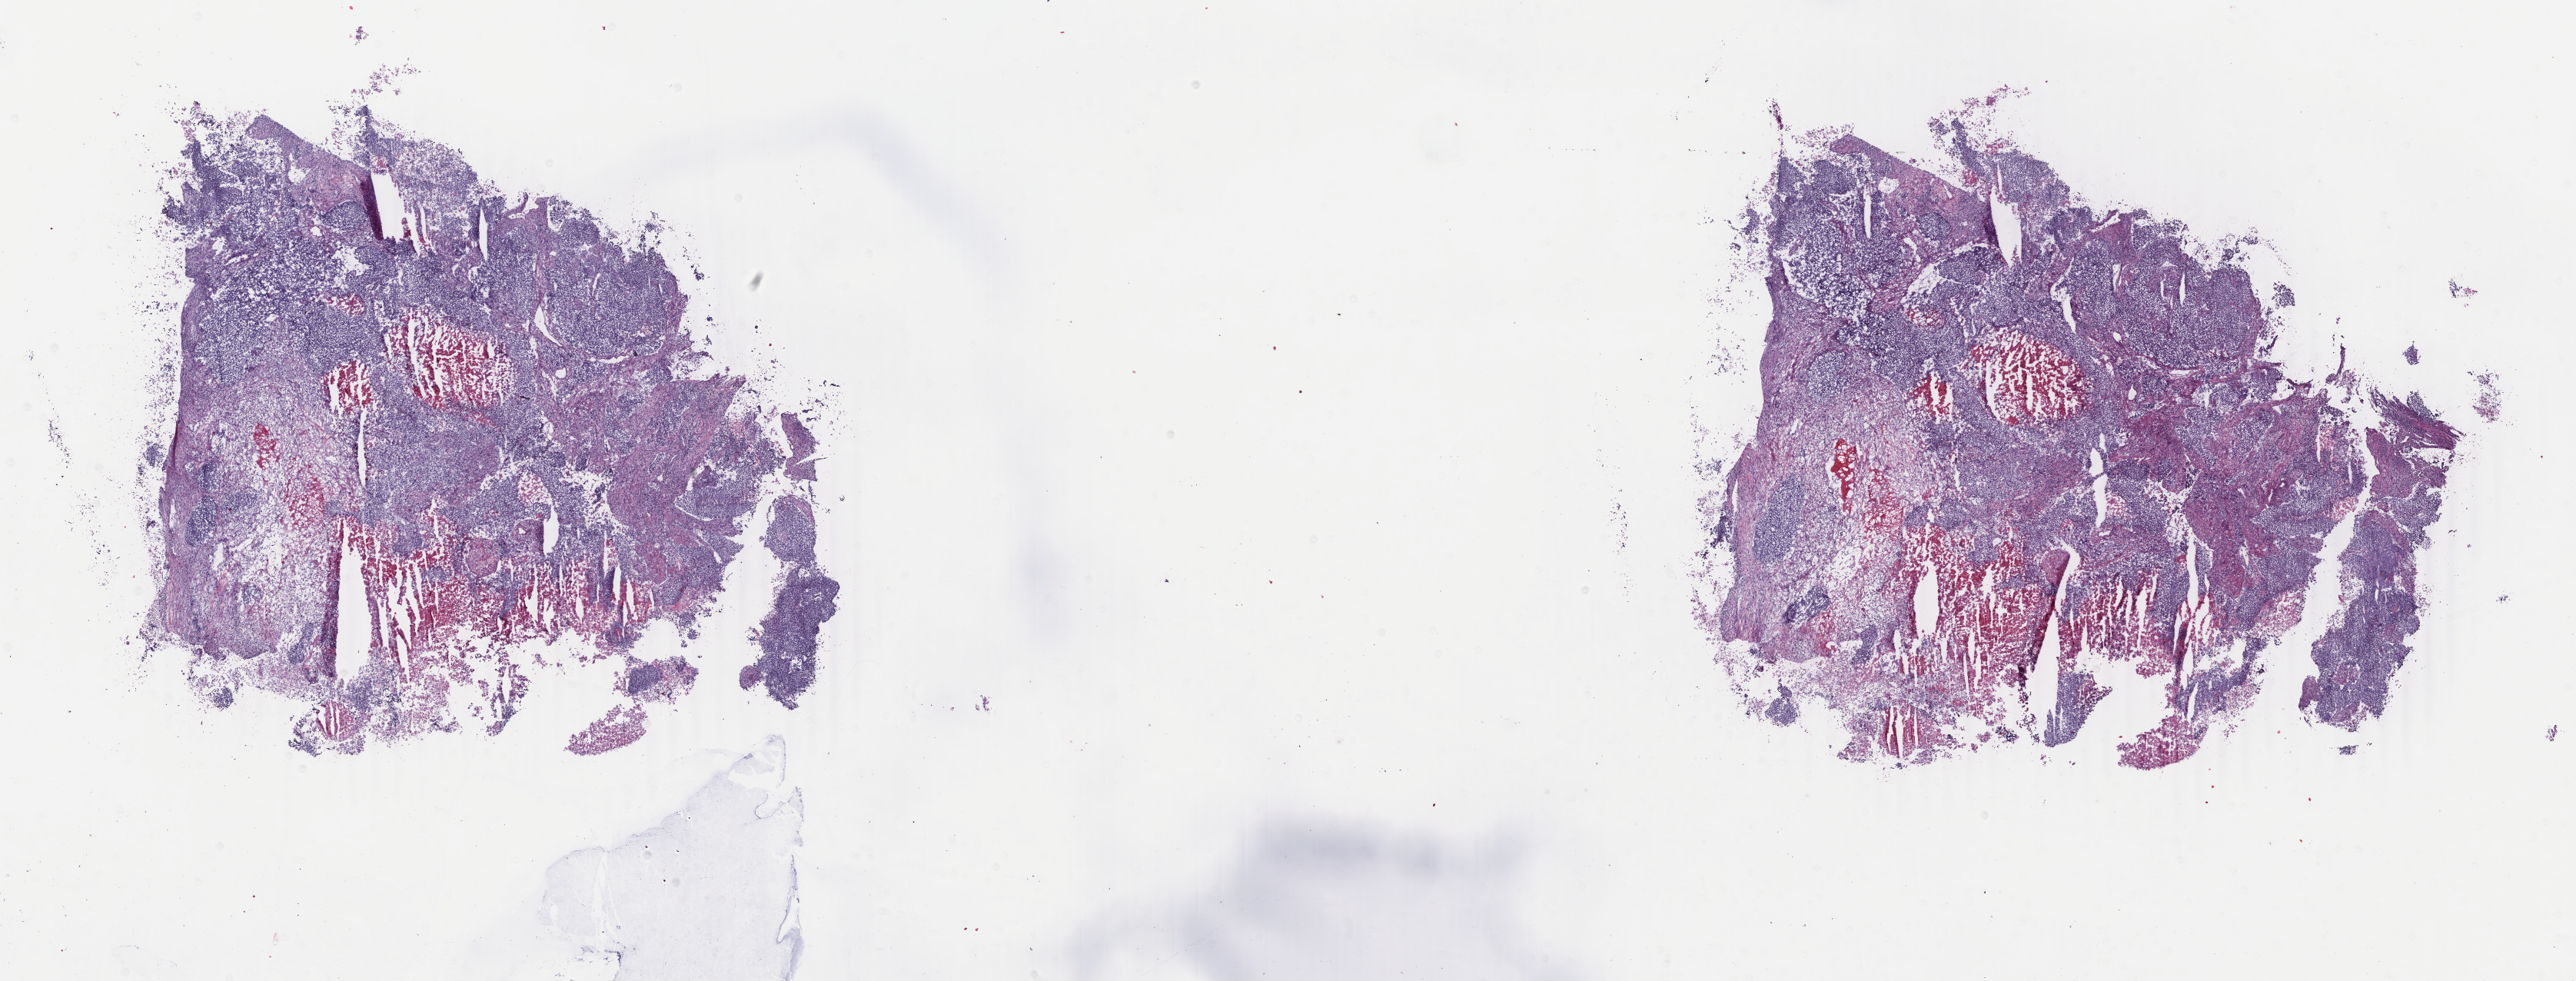
Digitized H&E-stained tissue section (whole slide) — shown as a low-resolution overview of the whole scanned area (about 26.7 x 10.1 mm), frozen section from the top of the tissue portion, uterus, primary tumour sample. Female, age 50 years at initial diagnosis. Histologic grade: G3 (poorly differentiated). Slide review estimates, as recorded: tumour cells 40%, tumour nuclei 70%, normal cells 30%, stromal cells 0%, necrosis 30%. Infiltration values recorded for this section: lymphocyte infiltration 20%, monocyte infiltration 0%, neutrophil infiltration 10%.
Histologic diagnosis: Carcinoma, undifferentiated, NOS (endometrium). FIGO stage: IIIC1.